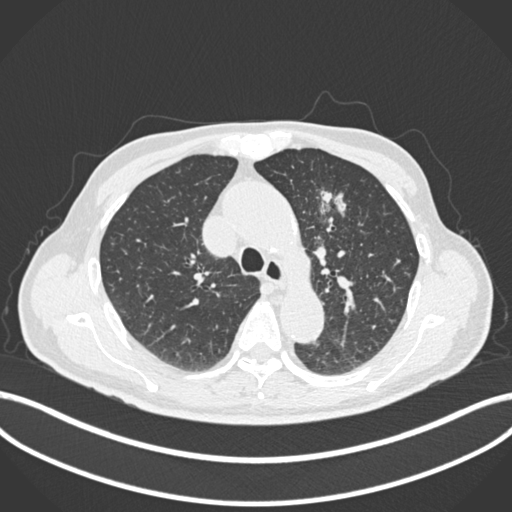
Chest CT, one axial slice. Position 175 of 261 along the scan axis. Reconstruction kernel B30f. Lung window (W 1500 / L -600 HU). 1 mm slice thickness. 512 × 512 image matrix, field of view 400 × 400 mm. Patient: male, 74 years. Case-level facts recorded for this patient, not image findings: clinical TNM (as recorded): T2b N0 M1c.
Structures marked on this image (bounding box drawn by a radiologist):
- lung tumour (recorded histology: adenocarcinoma): box from (x=310, y=186) to (x=355, y=221) px